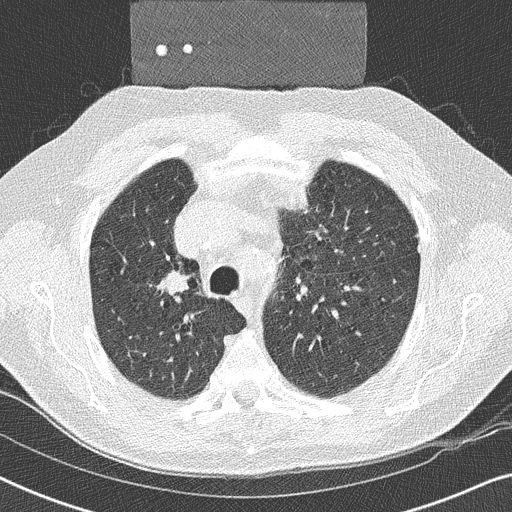
Low-dose screening chest CT, one axial slice; slice 179 of 252 in the series (ordered by position); lung window (W 1500 / L -600 HU); 512 × 512 image matrix, field of view 330 × 330 mm.
Outlined on this slice (outlined manually by an expert reader):
- lesion 1 (tumor, upper lobe of right lung): bounding box (x1, y1, x2, y2) in pixels: (165, 271, 186, 289)